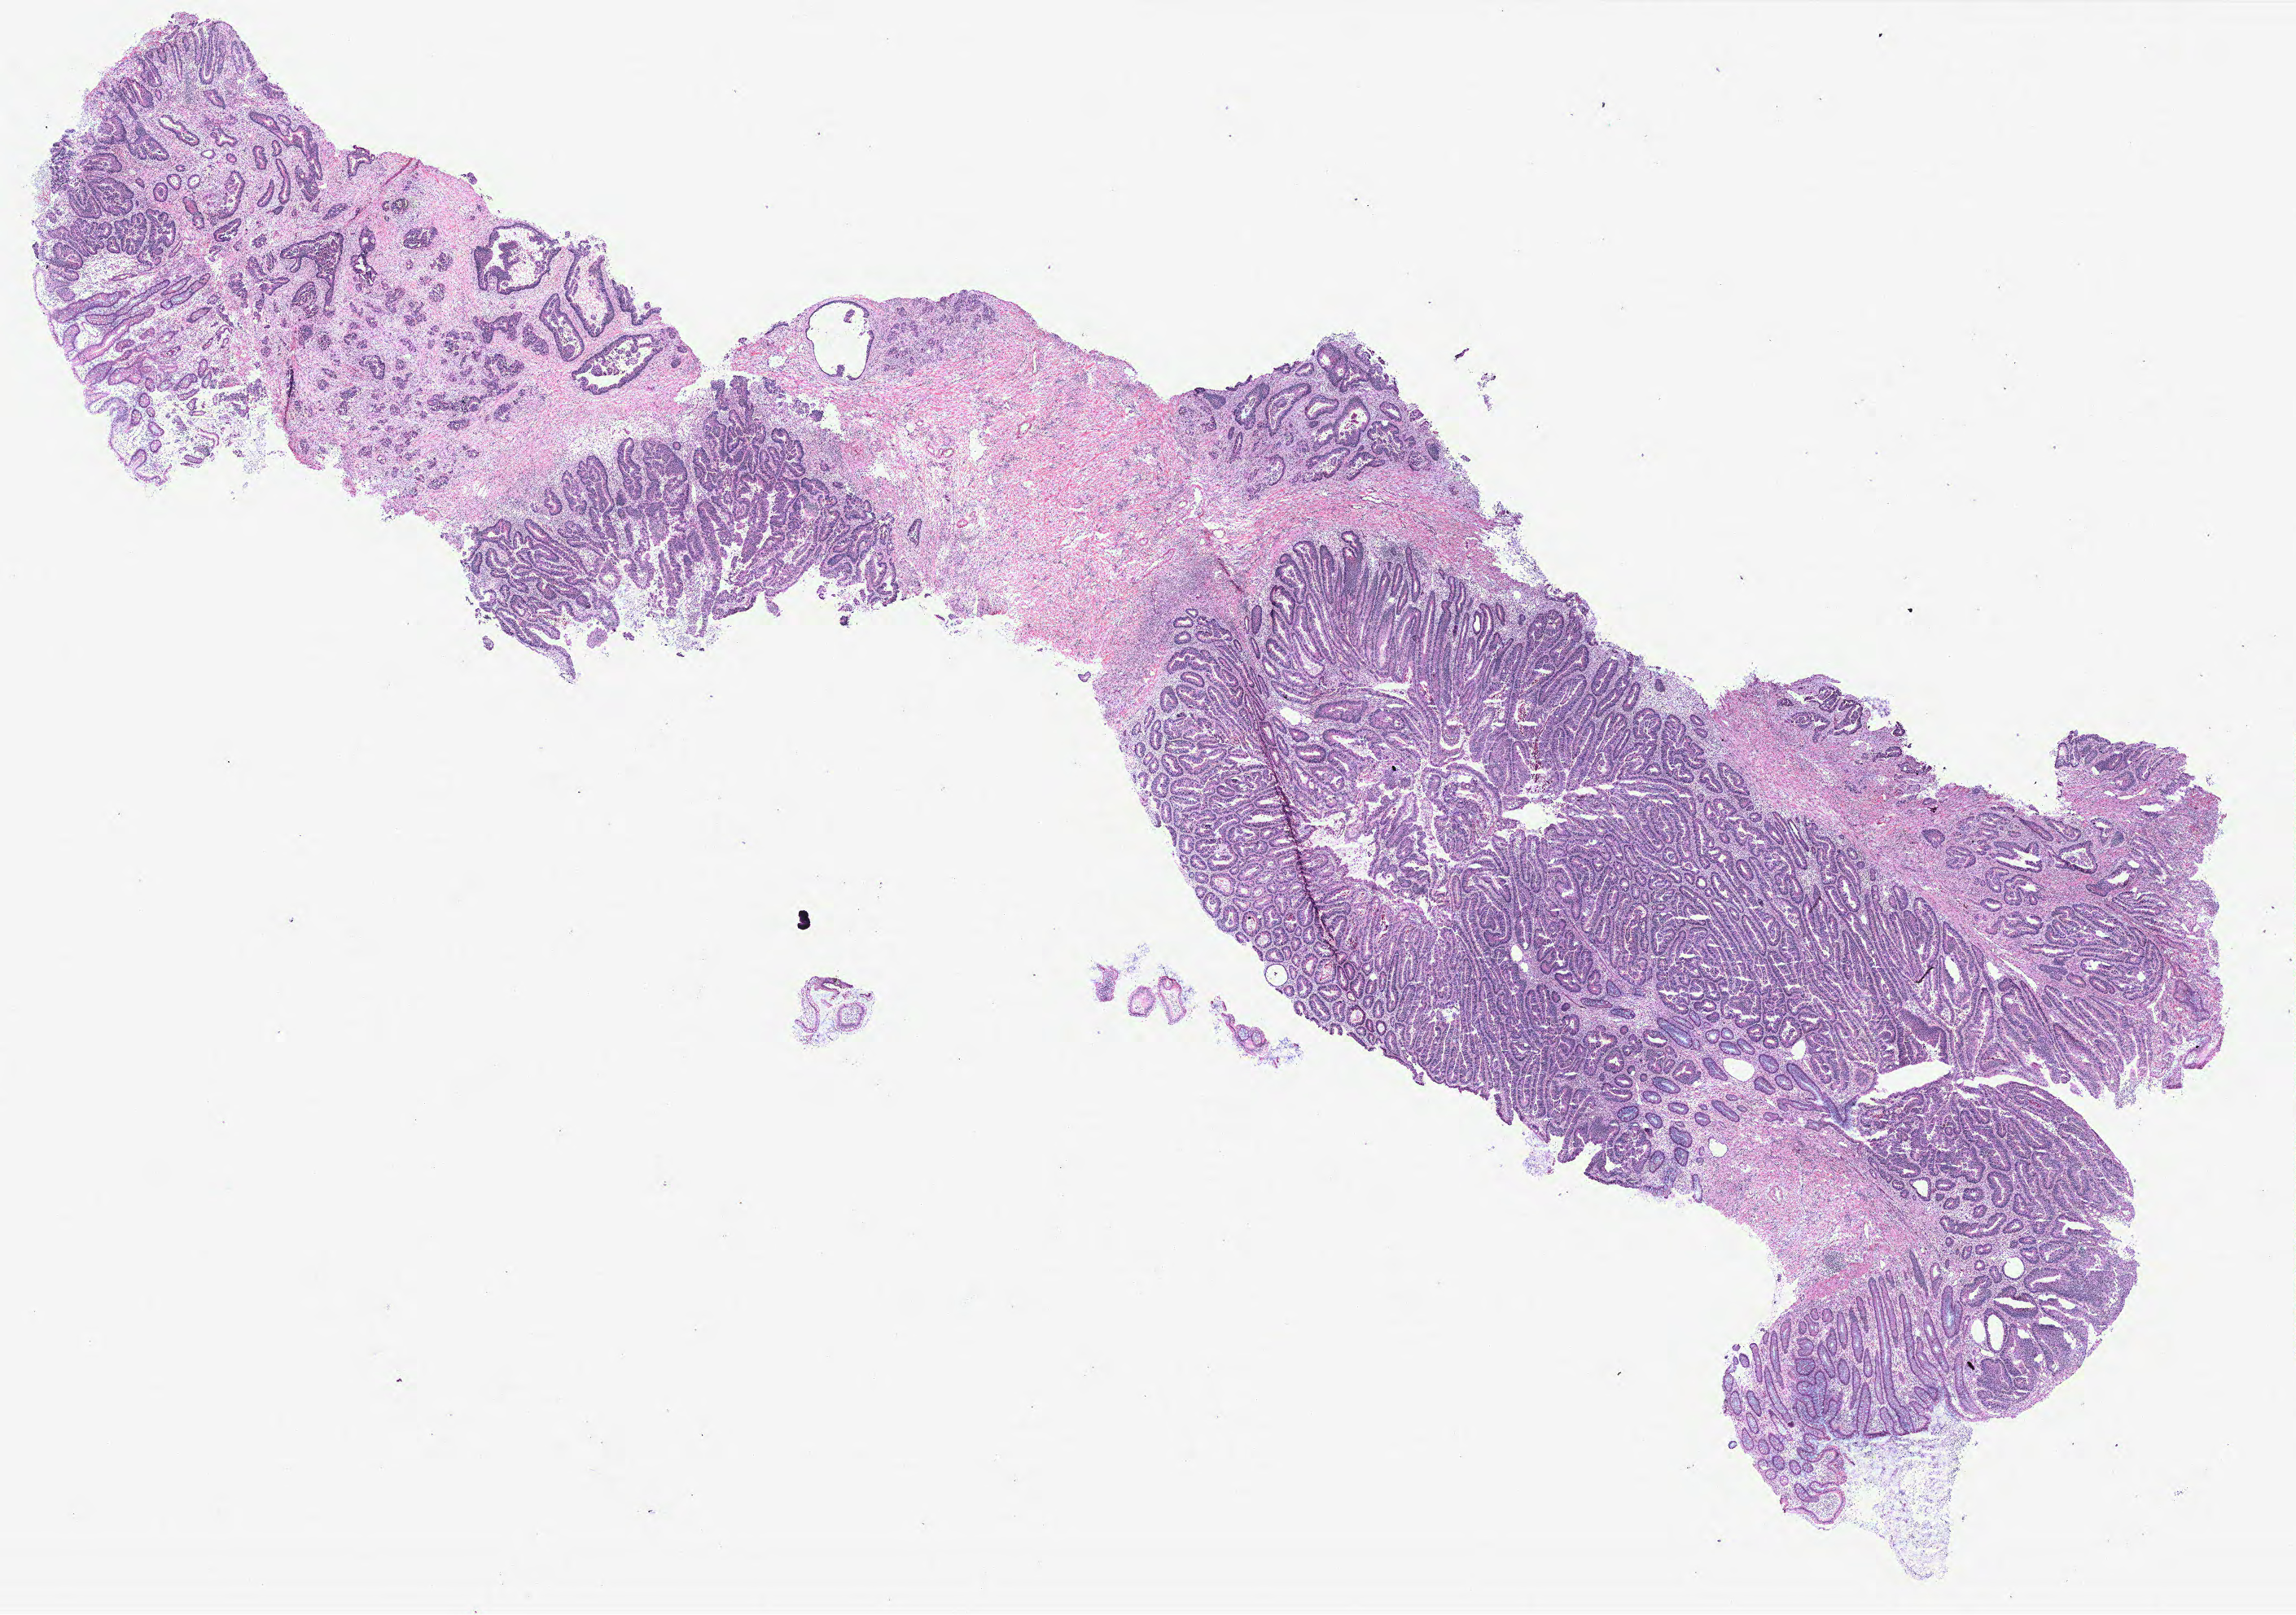
Whole-slide histology image, H&E-stained, a low-resolution overview of the entire scanned area, about 22.6 x 15.9 mm (from a 40x scan), colon, normal (non-tumour) tissue. Patient: male, age 68 years.
This section: normal (non-tumour) tissue from the same patient. Patient diagnosis: Adenocarcinoma, NOS.